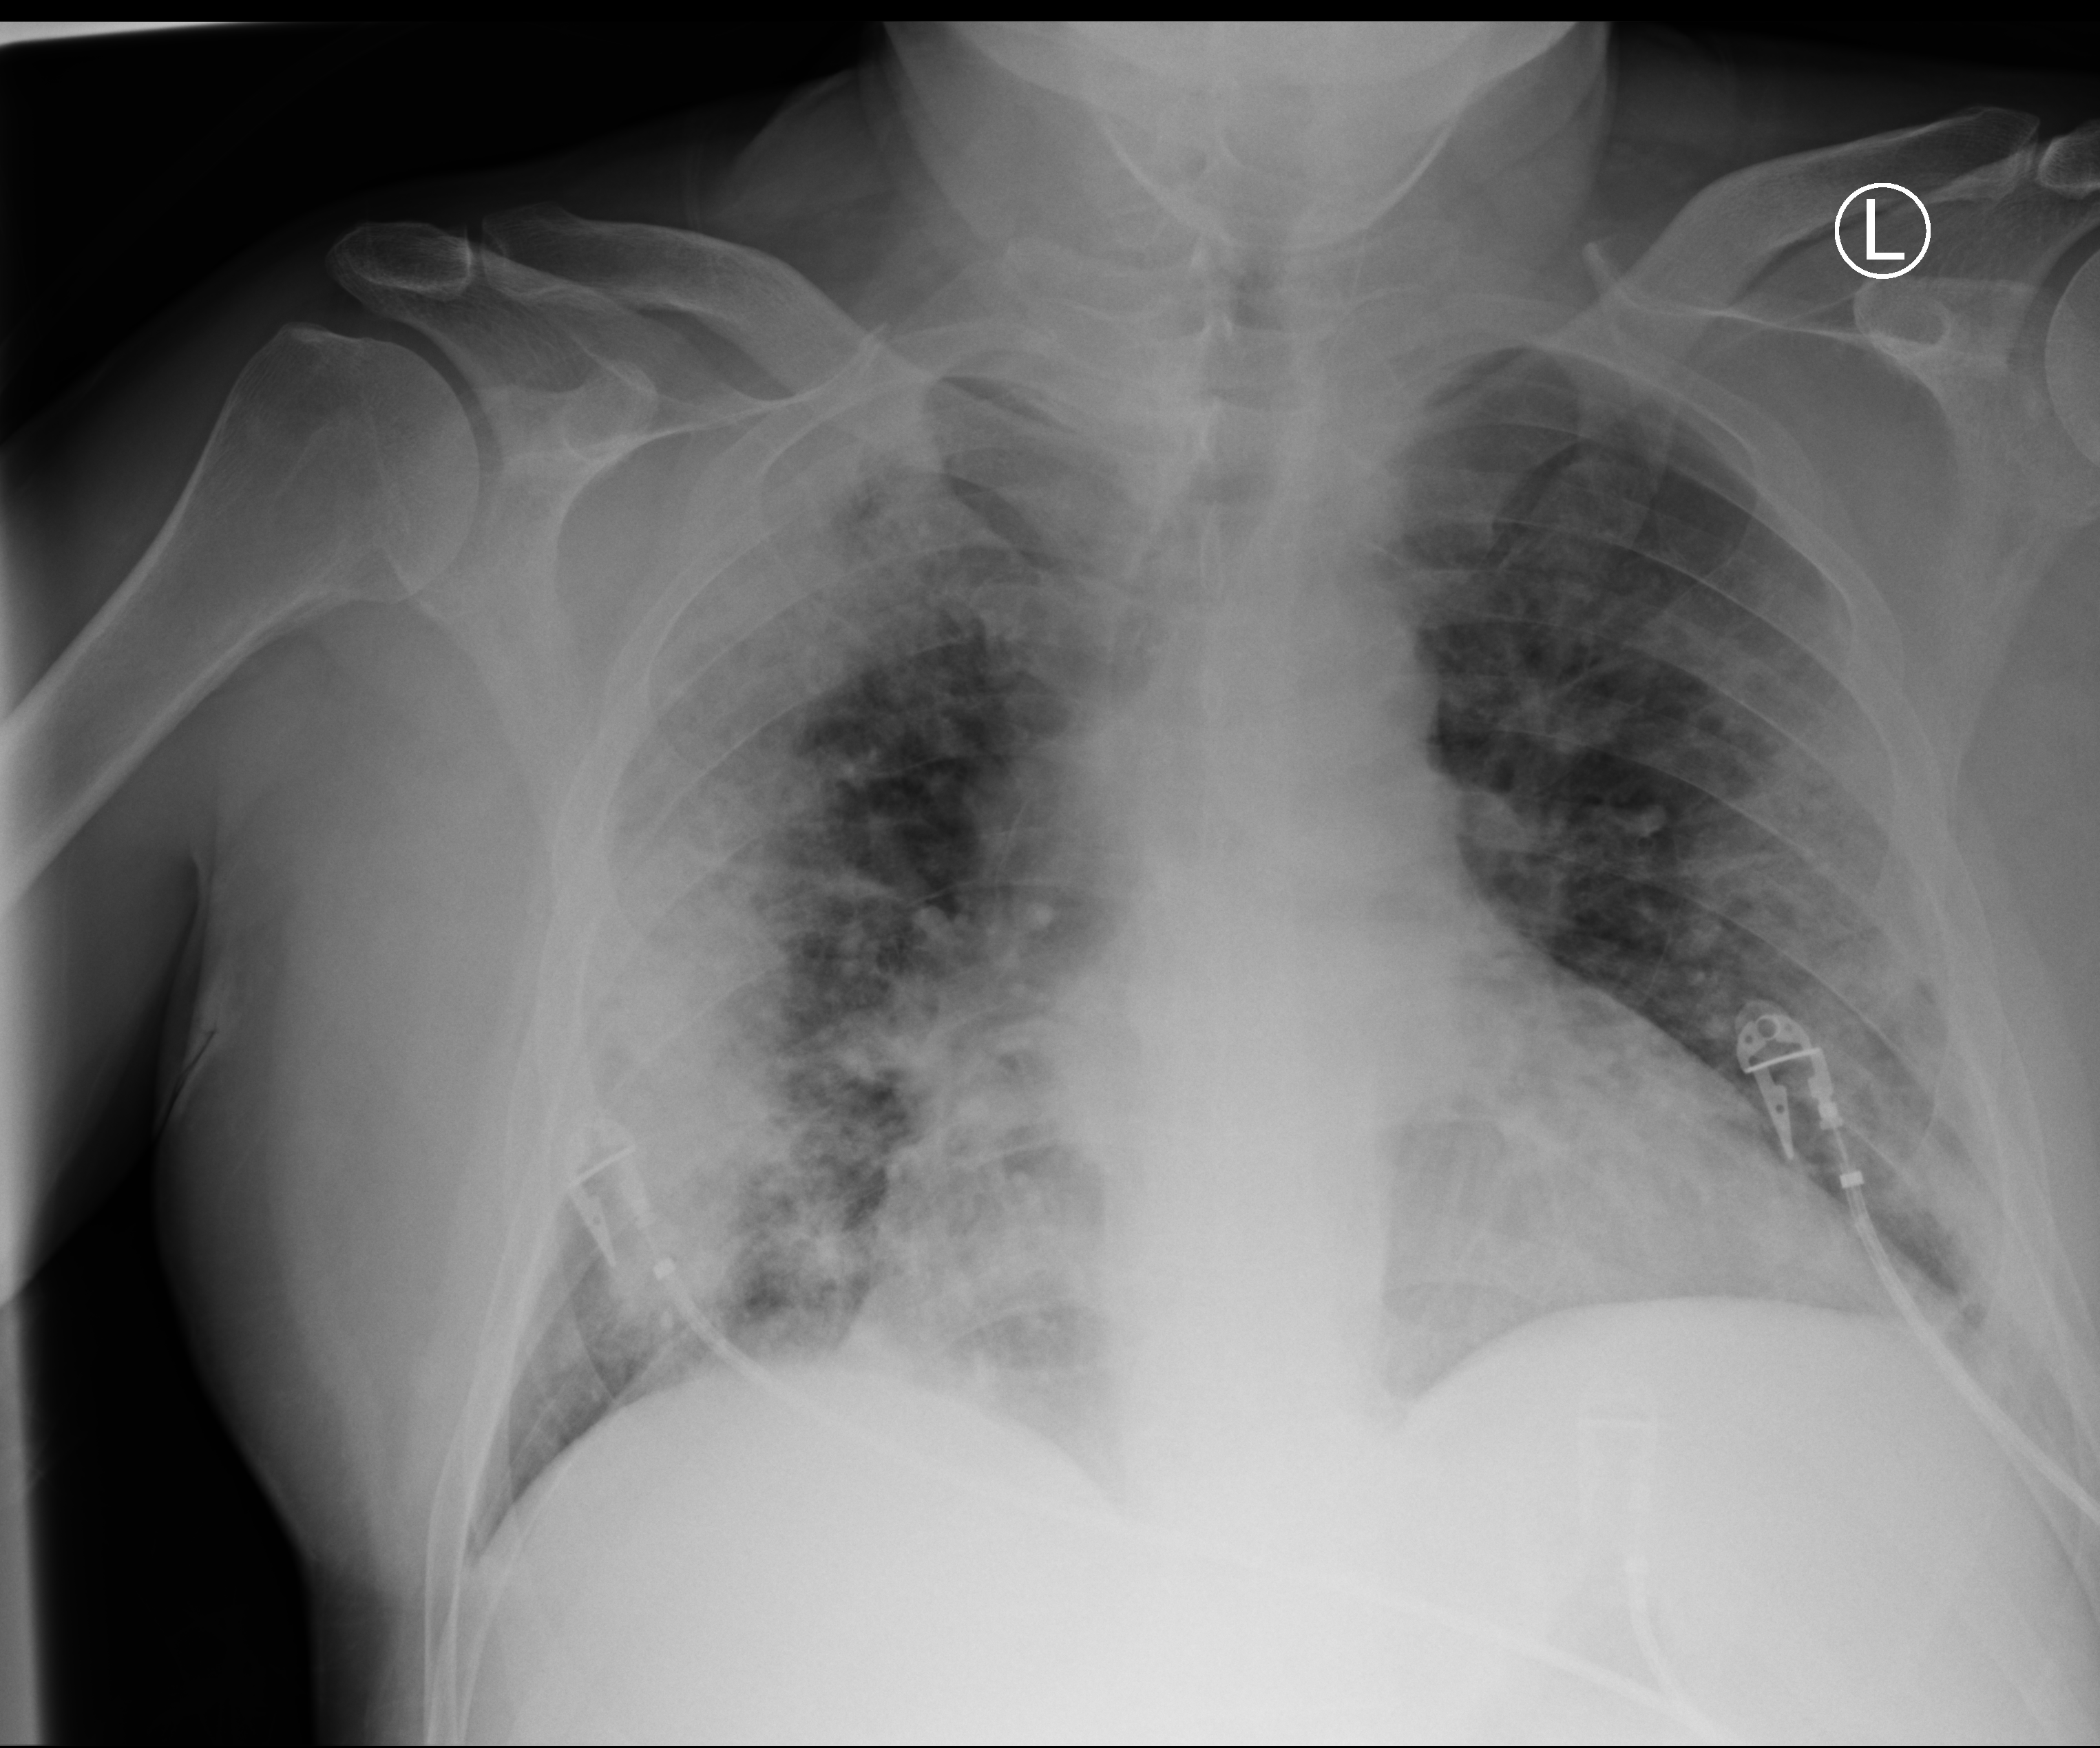
Chest X-ray (portable), anteroposterior (AP) projection. Patient hospitalised with COVID-19; male, aged 60–74 years.
Admission-level facts for this patient (not findings on this image; timing relative to this image not recorded): diabetes (admission record): no.